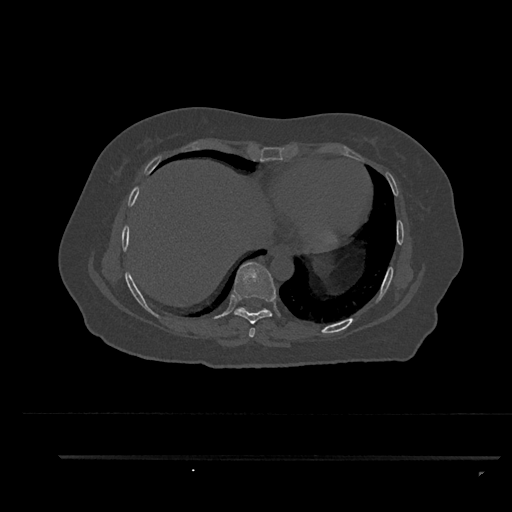
CT including the spine, one axial slice. Slice 452 of 797 in the series (ordered by position). Reconstruction kernel Br40s/3. 120 kVp. Bone window (W 1800 / L 400 HU). 0.5 mm slice thickness. 512 × 512 image matrix, field of view 408 × 408 mm. Patient: female, 44 years. From the clinical record (not read from this slice): primary cancer: renal; vertebrae with lytic lesions (as recorded): L1.
Annotated regions visible in this slice (semi-automatic segmentation, software-assisted and operator-edited):
- T7 vertebra: bounding box (x1, y1, x2, y2) in pixels: (249, 328, 255, 337)
- T8 vertebra: (233, 262, 276, 324)
- T9 vertebra: (235, 308, 268, 313)